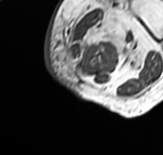
MRI of an extremity soft-tissue mass, one axial slice; slice 6 of 65 in the series (ordered by position); MR volume resampled by the dataset authors to the PET/CT grid (not the native acquisition matrix); 163 × 155 image matrix, field of view 159 × 151 mm. Female patient. Case-level facts recorded for this patient, not image findings: histological type: pleomorphic leiomyosarcoma; grade: high; site of the primary tumour: left thigh.
Structures marked on this image (expert contour drawn on MRI and transferred to this co-registered scan by the dataset authors):
- gross tumour volume including surrounding oedema: bounding box <65,6,147,71> (left, top, right, bottom; pixels)